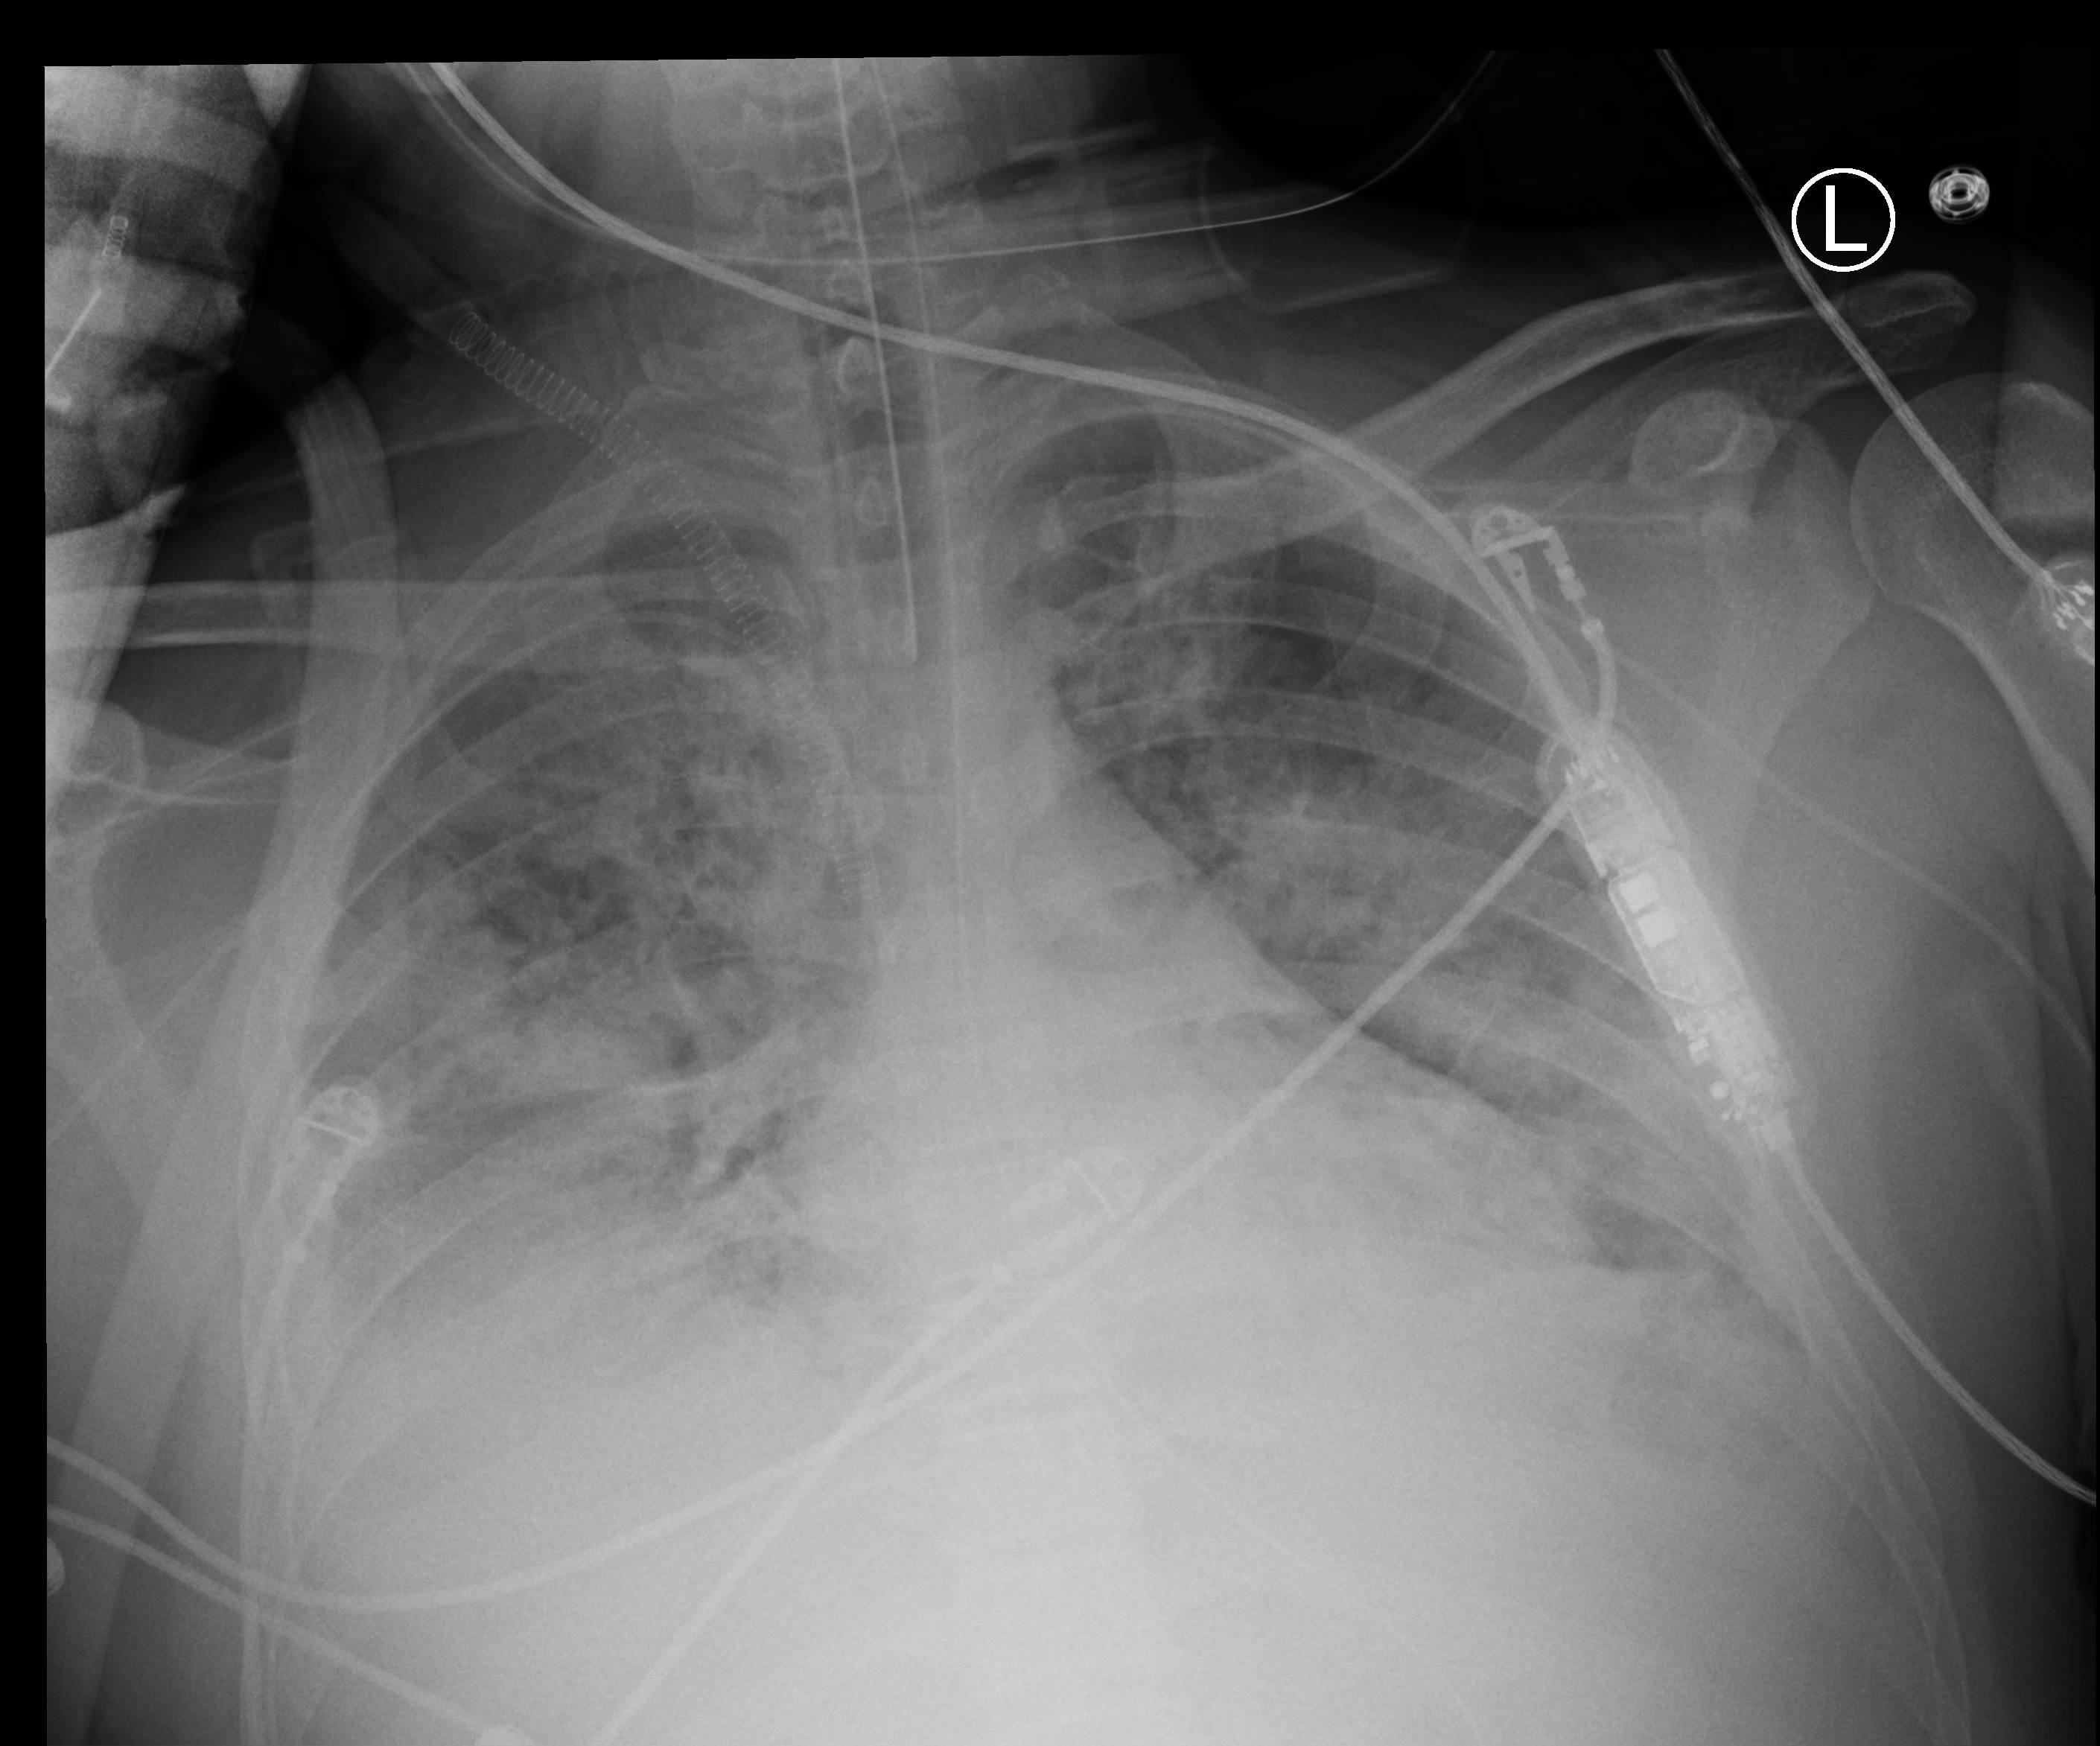
Portable chest radiograph, anteroposterior (AP) projection. Patient hospitalised with COVID-19, aged 18–59 years.
Admission-level facts for this patient (not findings on this image; timing relative to this image not recorded): length of hospital stay: 60 days.